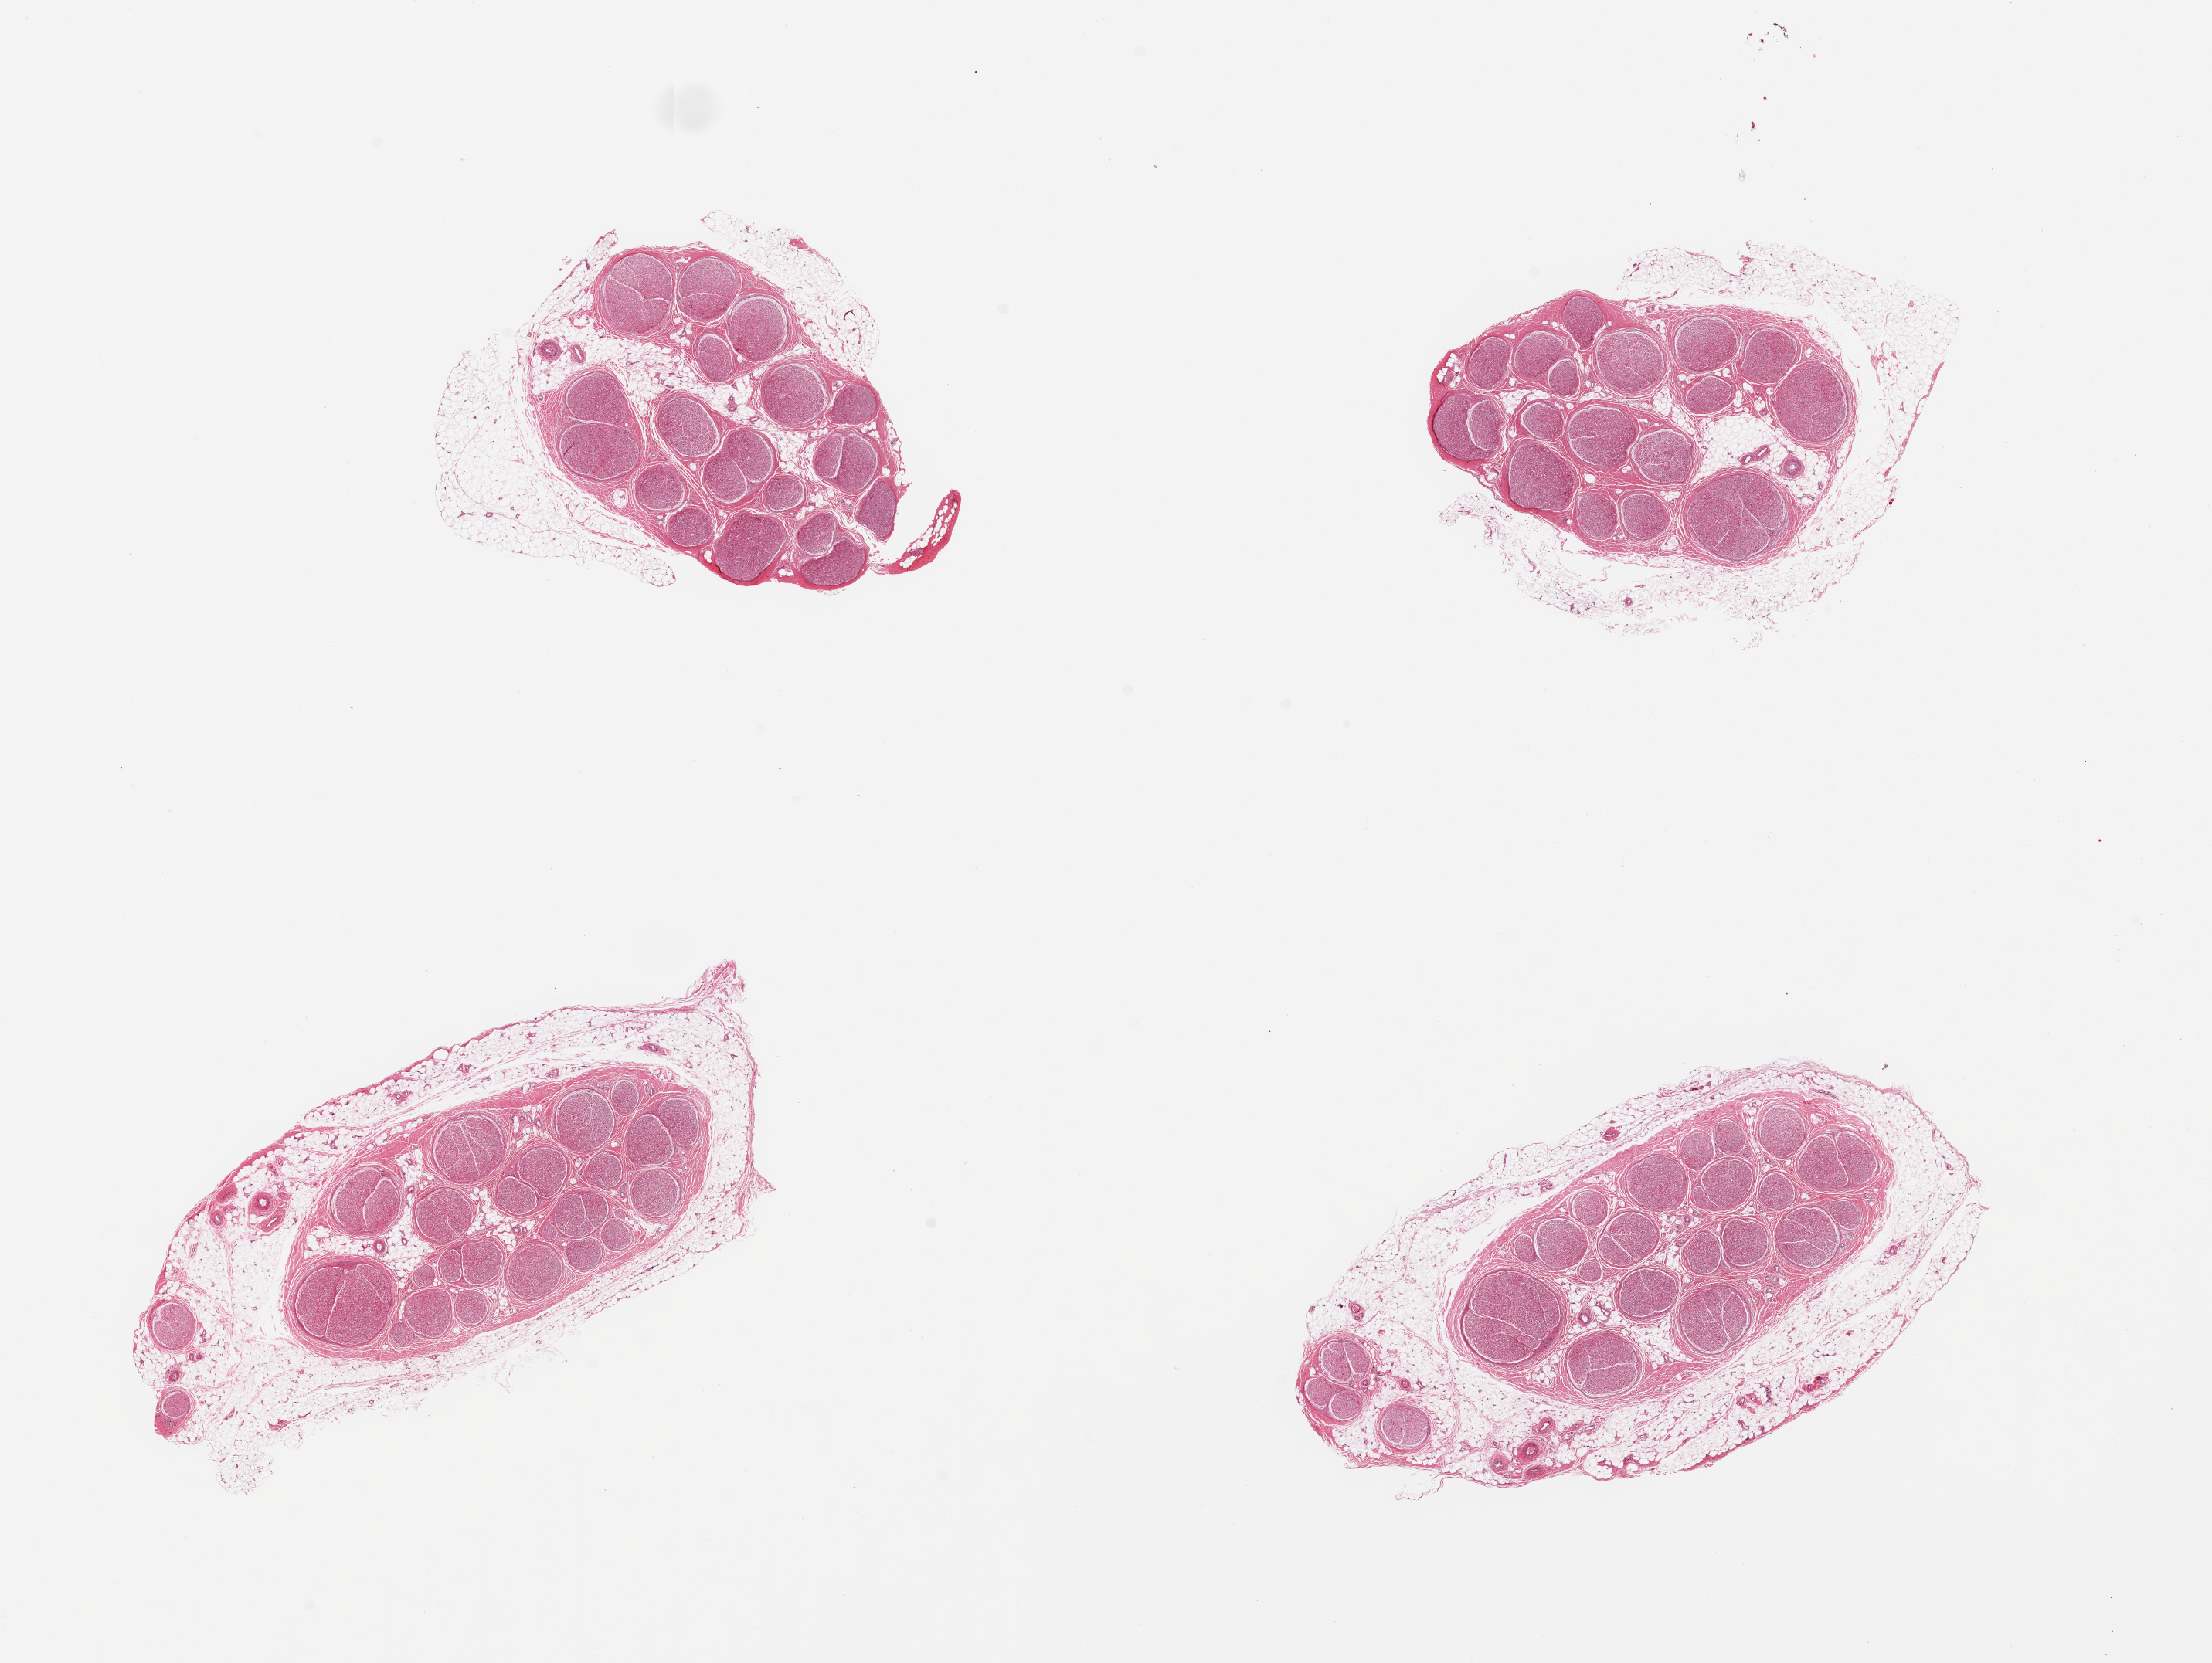
Whole-slide image, H&E stain, shown as a low-resolution overview of the whole scanned area (about 22.6 x 17.0 mm, acquisition: 20x scan); PAXgene-fixed, paraffin-embedded tissue; sampled site (target tissue): tibial nerve; donor tissue sample. Donor sex: male.
- reviewer comment on this tissue sample: 2 pieces; all with external fat up to 1 mm thick